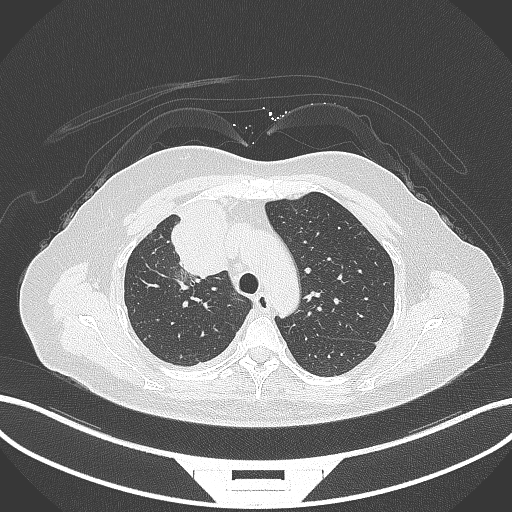
Chest CT, one axial slice. Position 217 of 305 along the scan axis. 120 kVp. Lung window (W 1500 / L -600 HU). 1 mm slice thickness. 512 × 512 image matrix, field of view 400 × 400 mm. Patient: female, 52 years. Case-level facts recorded for this patient, not image findings: clinical TNM (as recorded): T3 N1 M1.
Structures marked on this image (rectangle marked by the reading radiologist):
- lung tumour (recorded histology: adenocarcinoma): bounding box [x1, y1, x2, y2] px = [168, 198, 228, 278]